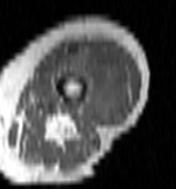
MRI of an extremity soft-tissue mass, one axial slice; slice 38 of 100 in the series (ordered by position); MR volume resampled by the dataset authors to the PET/CT grid (not the native acquisition matrix); 176 × 189 image matrix, field of view 172 × 185 mm. Female patient. From the clinical record (not read from this slice): histological type: undifferentiated – high grade; grade: high; site of the primary tumour: left thigh.
Outlined on this slice (expert contour drawn on MRI and transferred to this co-registered scan by the dataset authors):
- gross tumour volume including surrounding oedema: box from (x=60, y=45) to (x=129, y=122) px
- gross tumour volume (mass): (x=85, y=52)–(x=129, y=122)